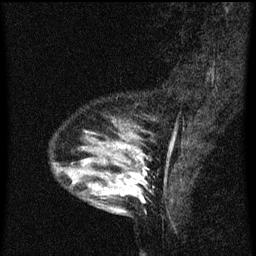
Breast MRI (dynamic contrast-enhanced), one sagittal slice. Slice 16 of 60 in the series (ordered by position). Dynamic contrast-enhanced series, image 2 of 3 at this slice position (ordered by acquisition). 1.5 T. TE 4.2 ms, TR 8 ms. 2 mm slice thickness. 256 × 256 image matrix, field of view 180 × 180 mm. Female patient, age 33 years.
Structures marked on this image (semi-automatically segmented with operator editing):
- analysis volume of interest (the breast-tissue region the enhancement analysis was run in; not a lesion): bounding box <61,126,147,213> (left, top, right, bottom; pixels)
- tumour enhancement mask (voxels above the 70 % enhancement threshold inside the analysis volume of interest): <107,146,144,197>